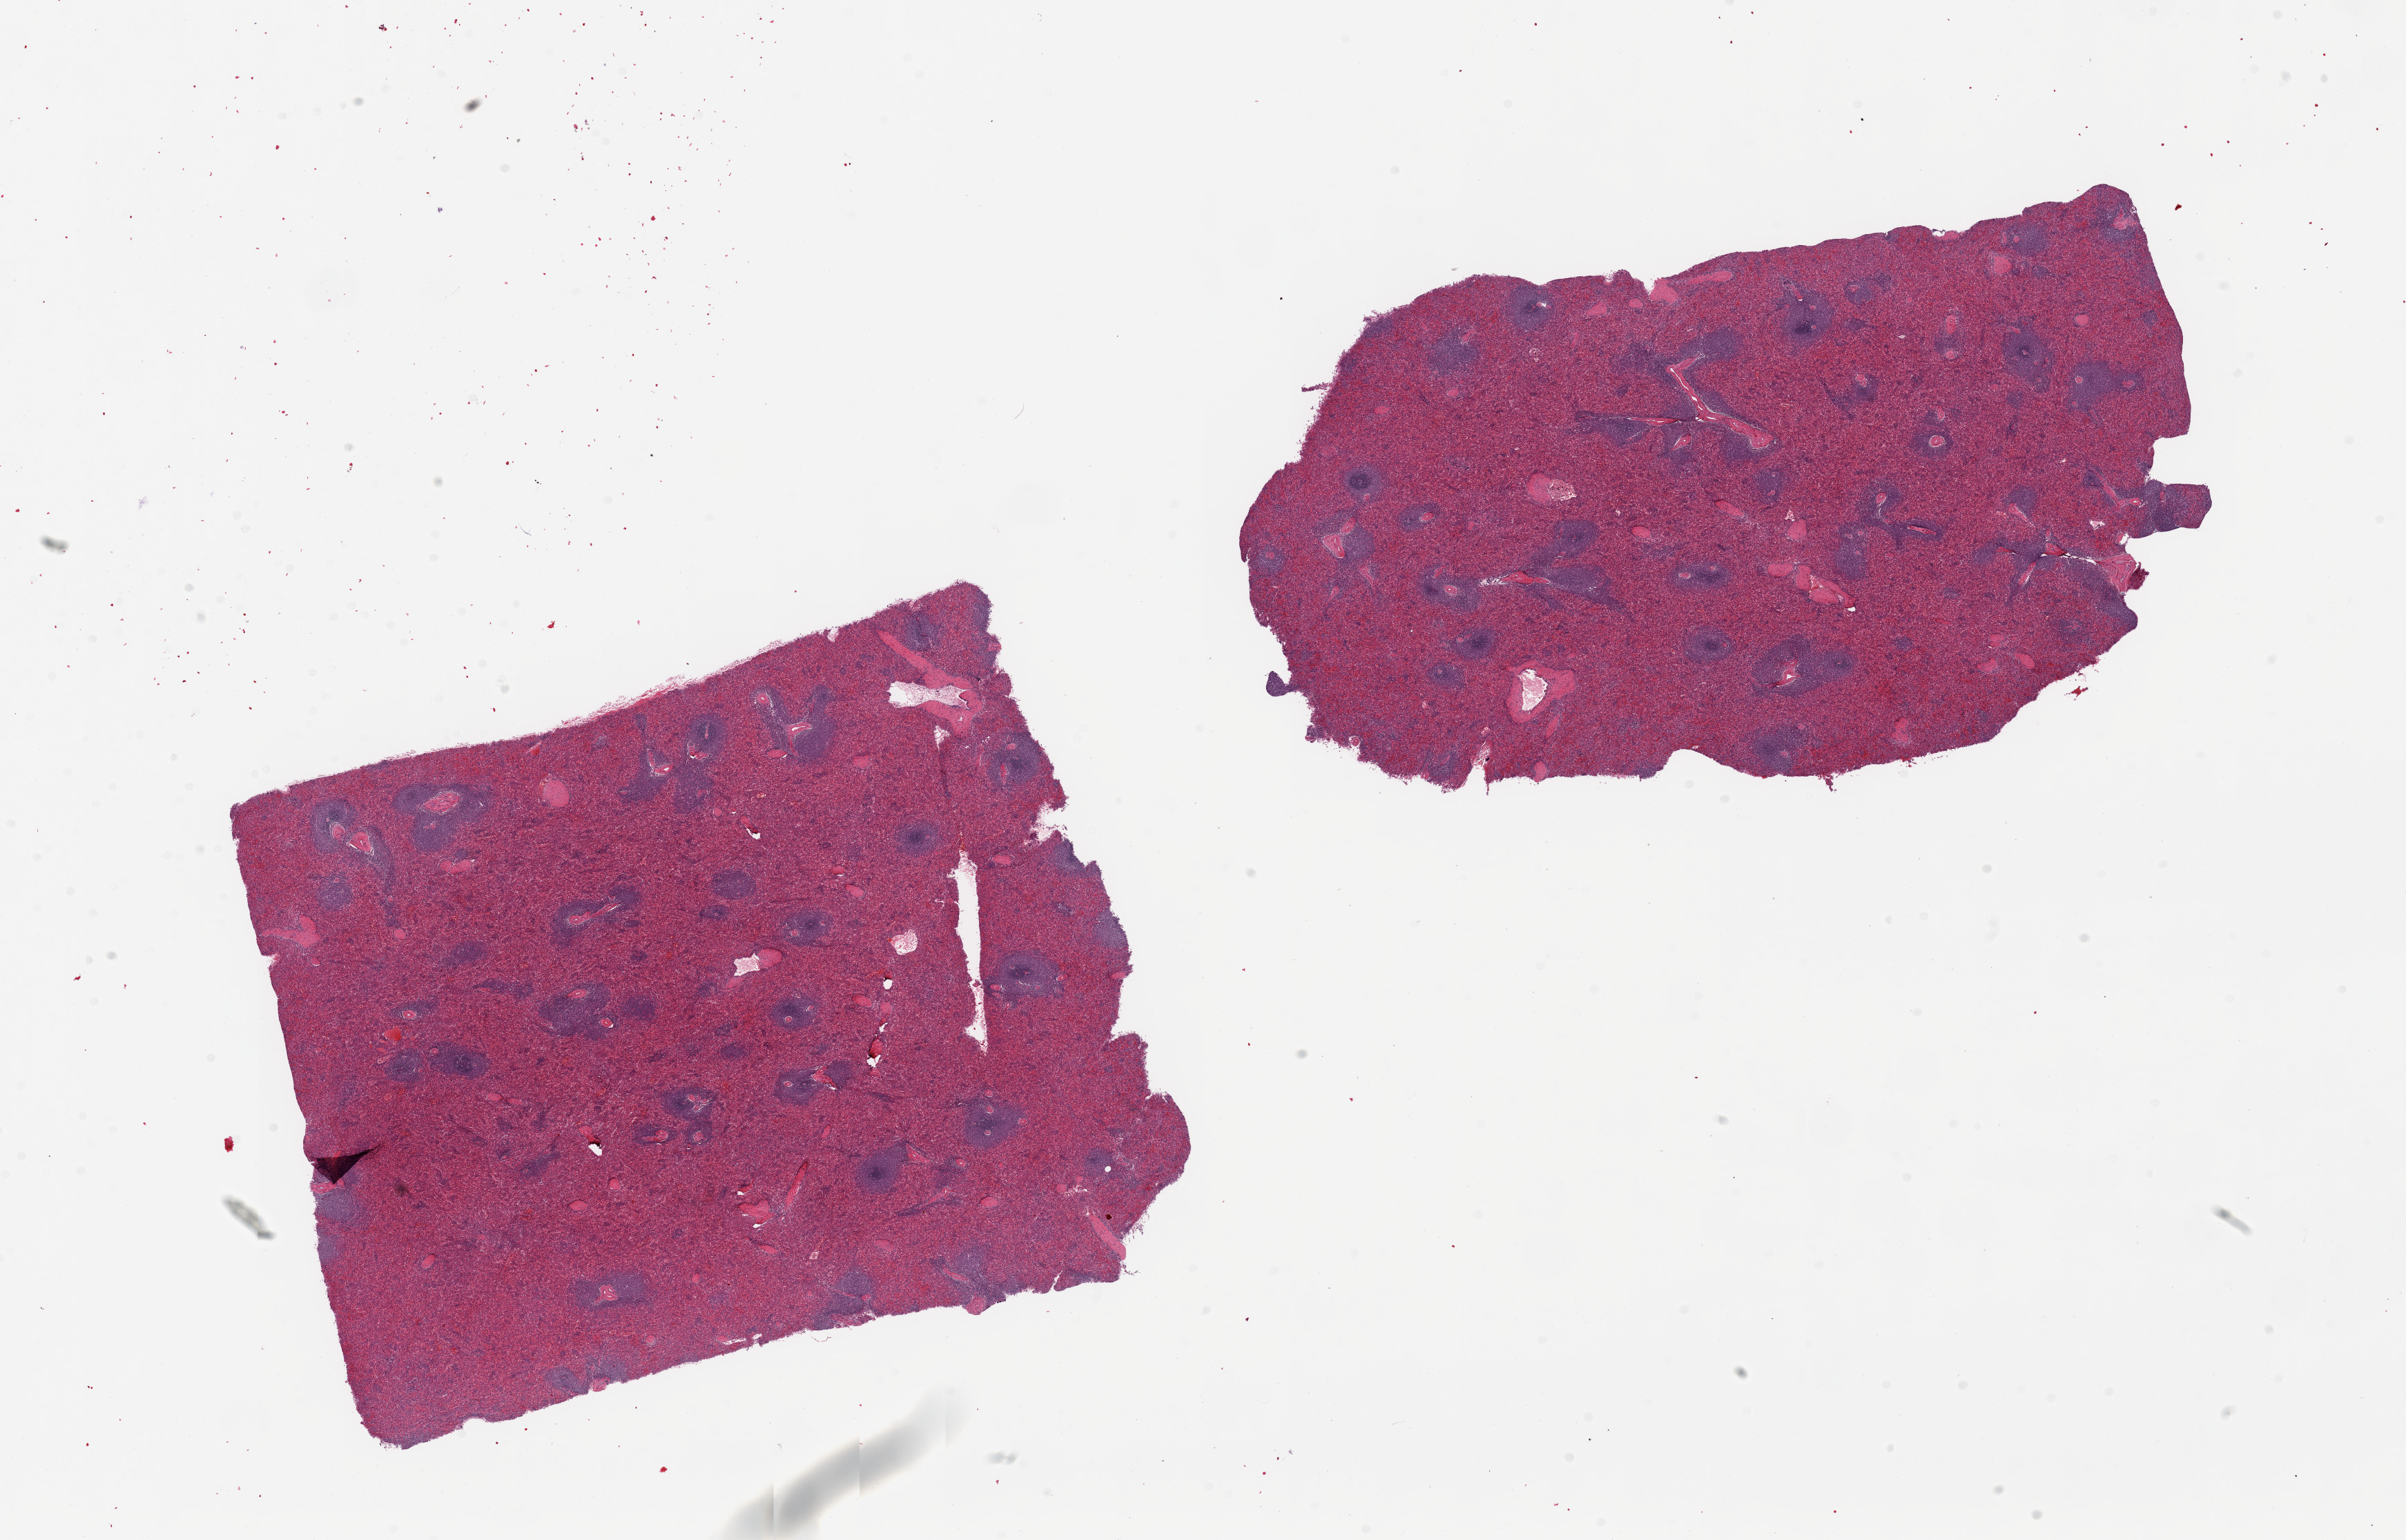
Whole-slide image, hematoxylin and eosin (H&E) stain — shown as a low-resolution overview of the whole scanned area (about 27.6 x 17.6 mm, from a 20x scan); PAXgene-fixed, paraffin-embedded tissue; sampled site (target tissue): spleen; donor tissue sample. Donor: male.
Review note (as recorded): 2 pieces, no abnormalities.